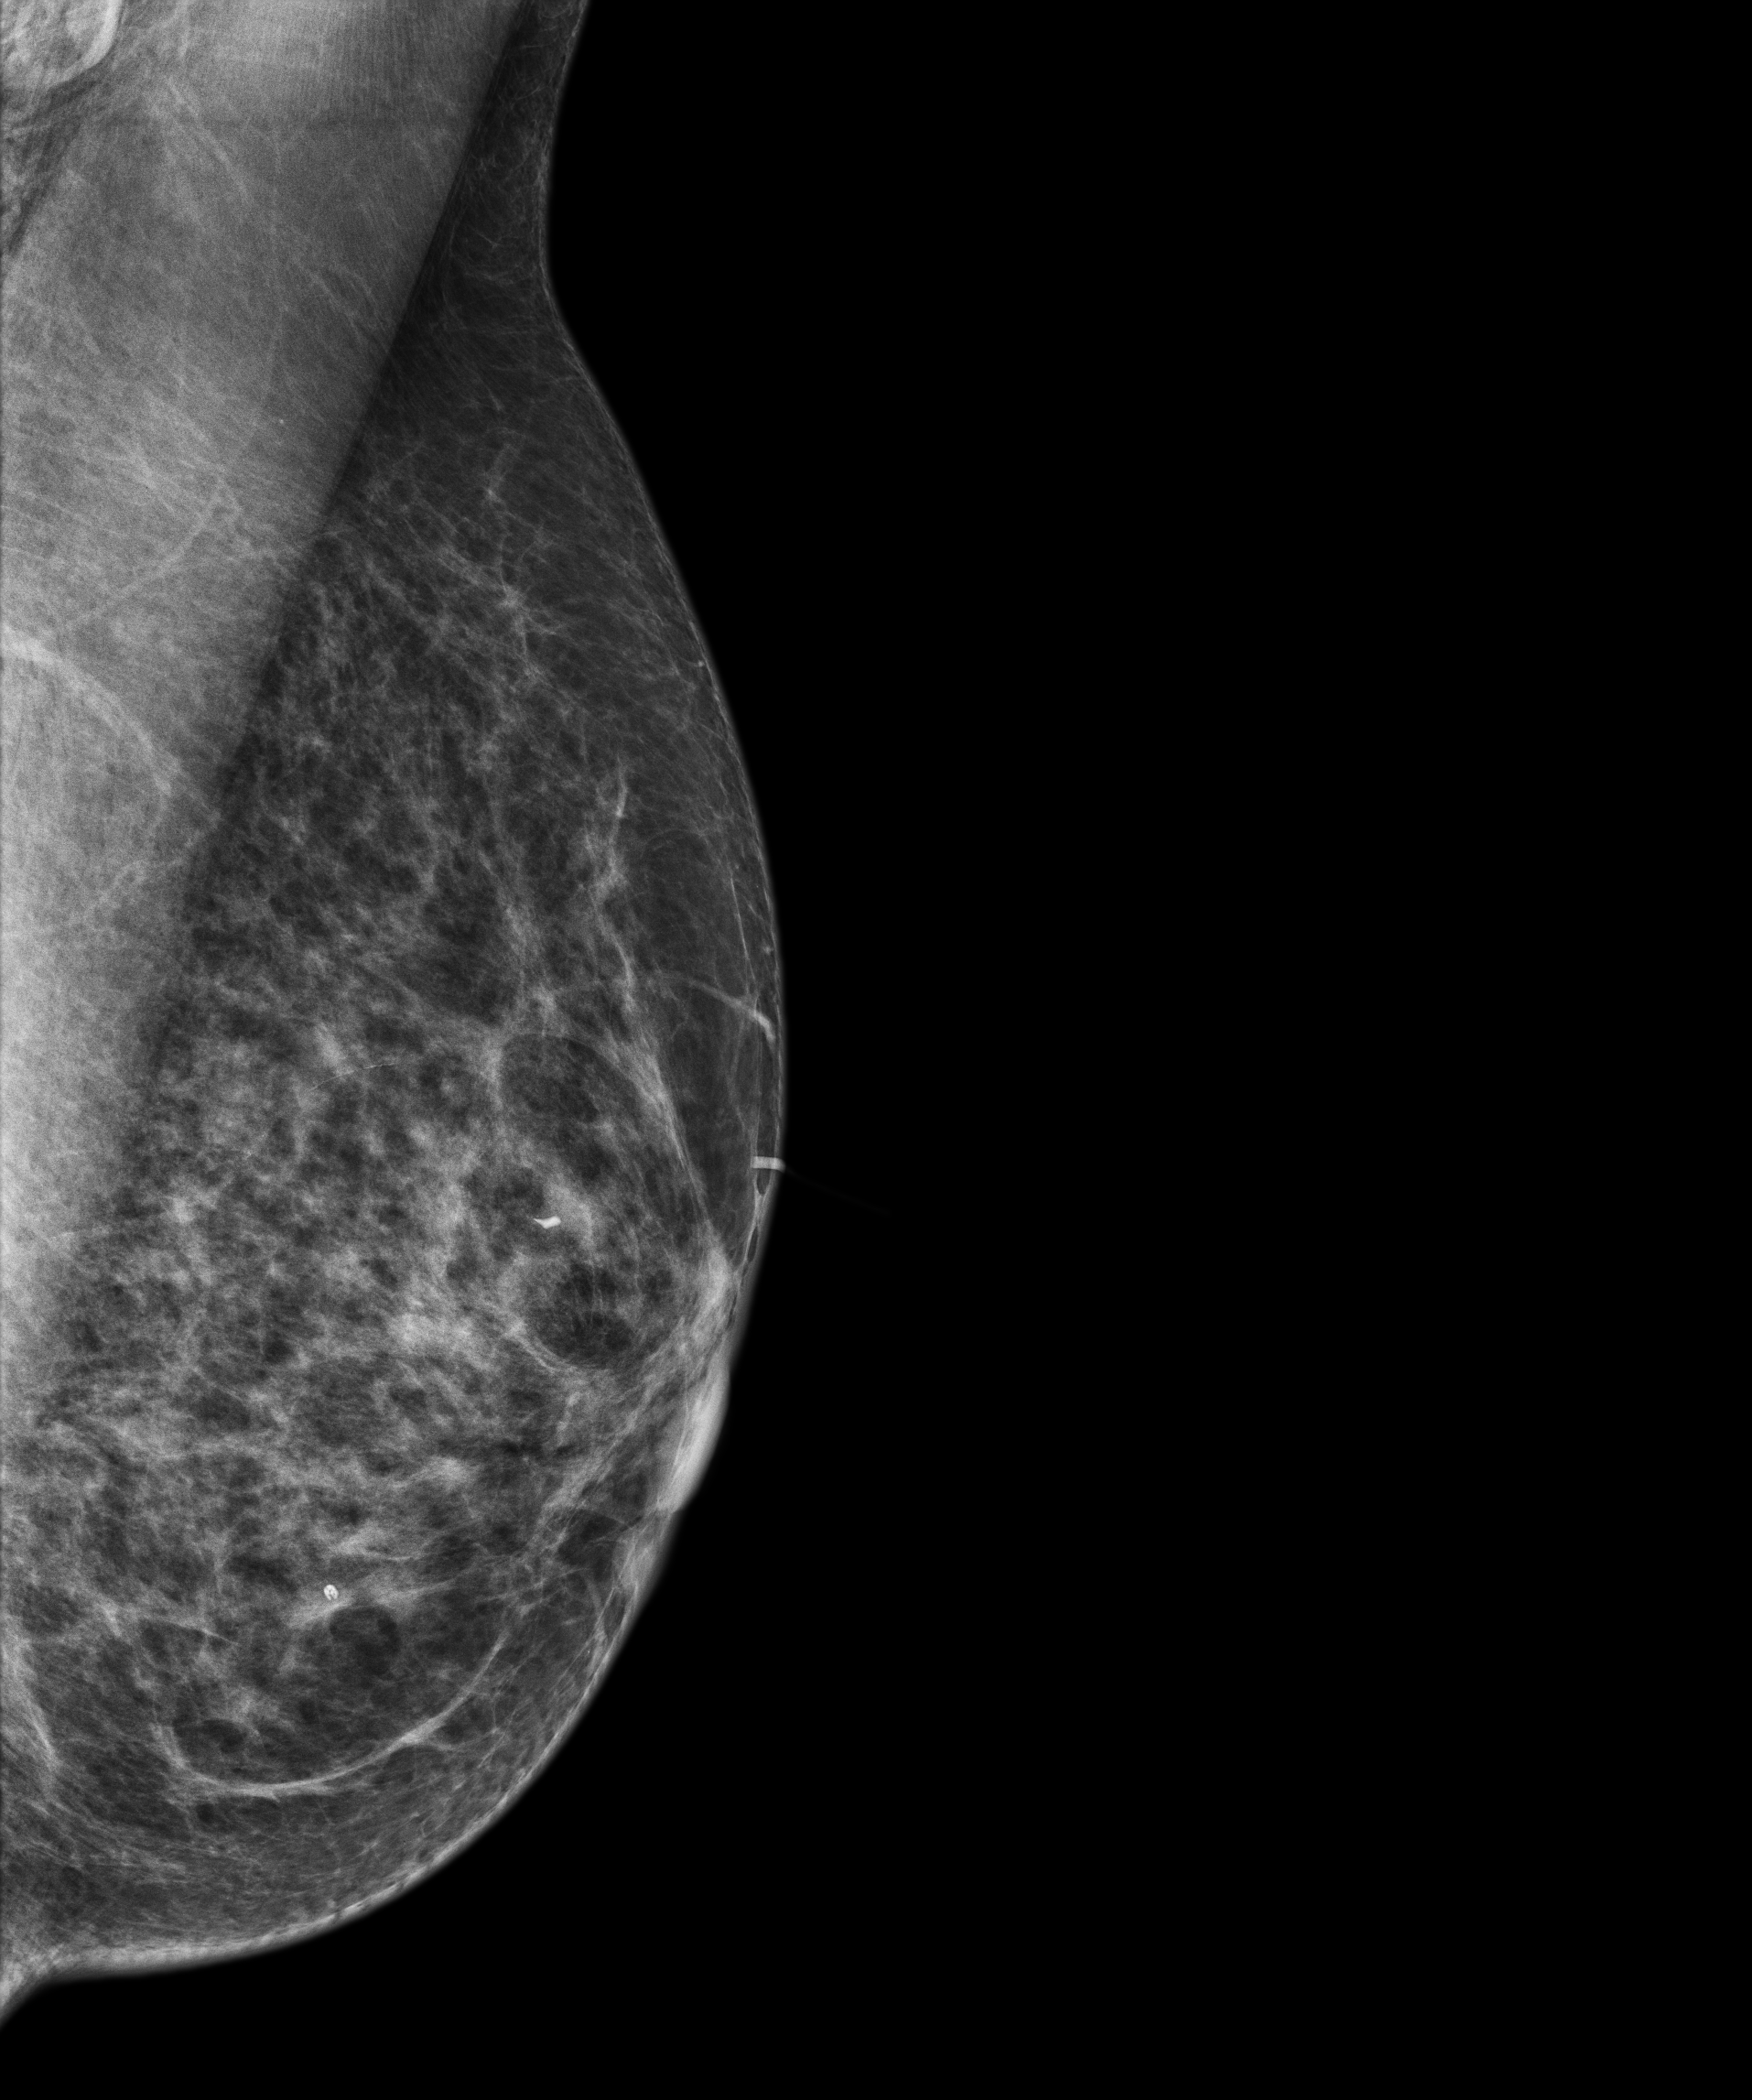
Full-field digital mammogram (FFDM); left breast; medio-lateral oblique projection; annual screening mammography examination; system: Senographe Essential ADS_56.21.3. Patient: female, 69 years.
- BI-RADS breast density category at the screening exam (both breasts, scale 1–4): 3
- final BI-RADS assessment for this screening round (tomosynthesis exam, both breasts): category 1
- recall: no recall after this screen